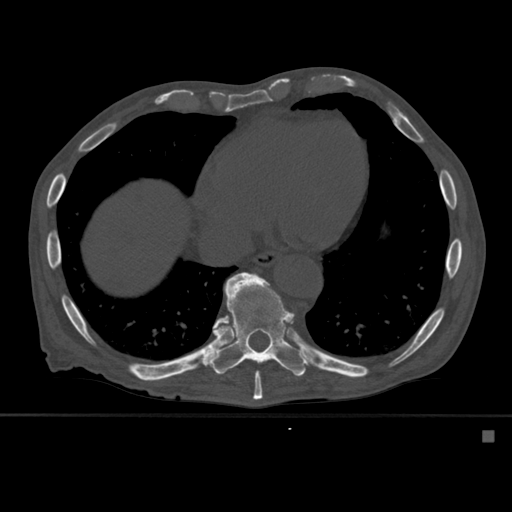
CT including the spine, one axial slice; bone window (W 1800 / L 400 HU); 1.5 mm slice thickness; 512 × 512 image matrix, field of view 373 × 373 mm. Male patient, age 78 years. From the clinical record (not read from this slice): primary cancer: prostate.
Structures marked on this image (semi-automatic segmentation, software-assisted and operator-edited):
- T10 vertebra: bounding box (x1, y1, x2, y2) in pixels: (208, 272, 308, 377)
- T9 vertebra: (230, 274, 291, 401)